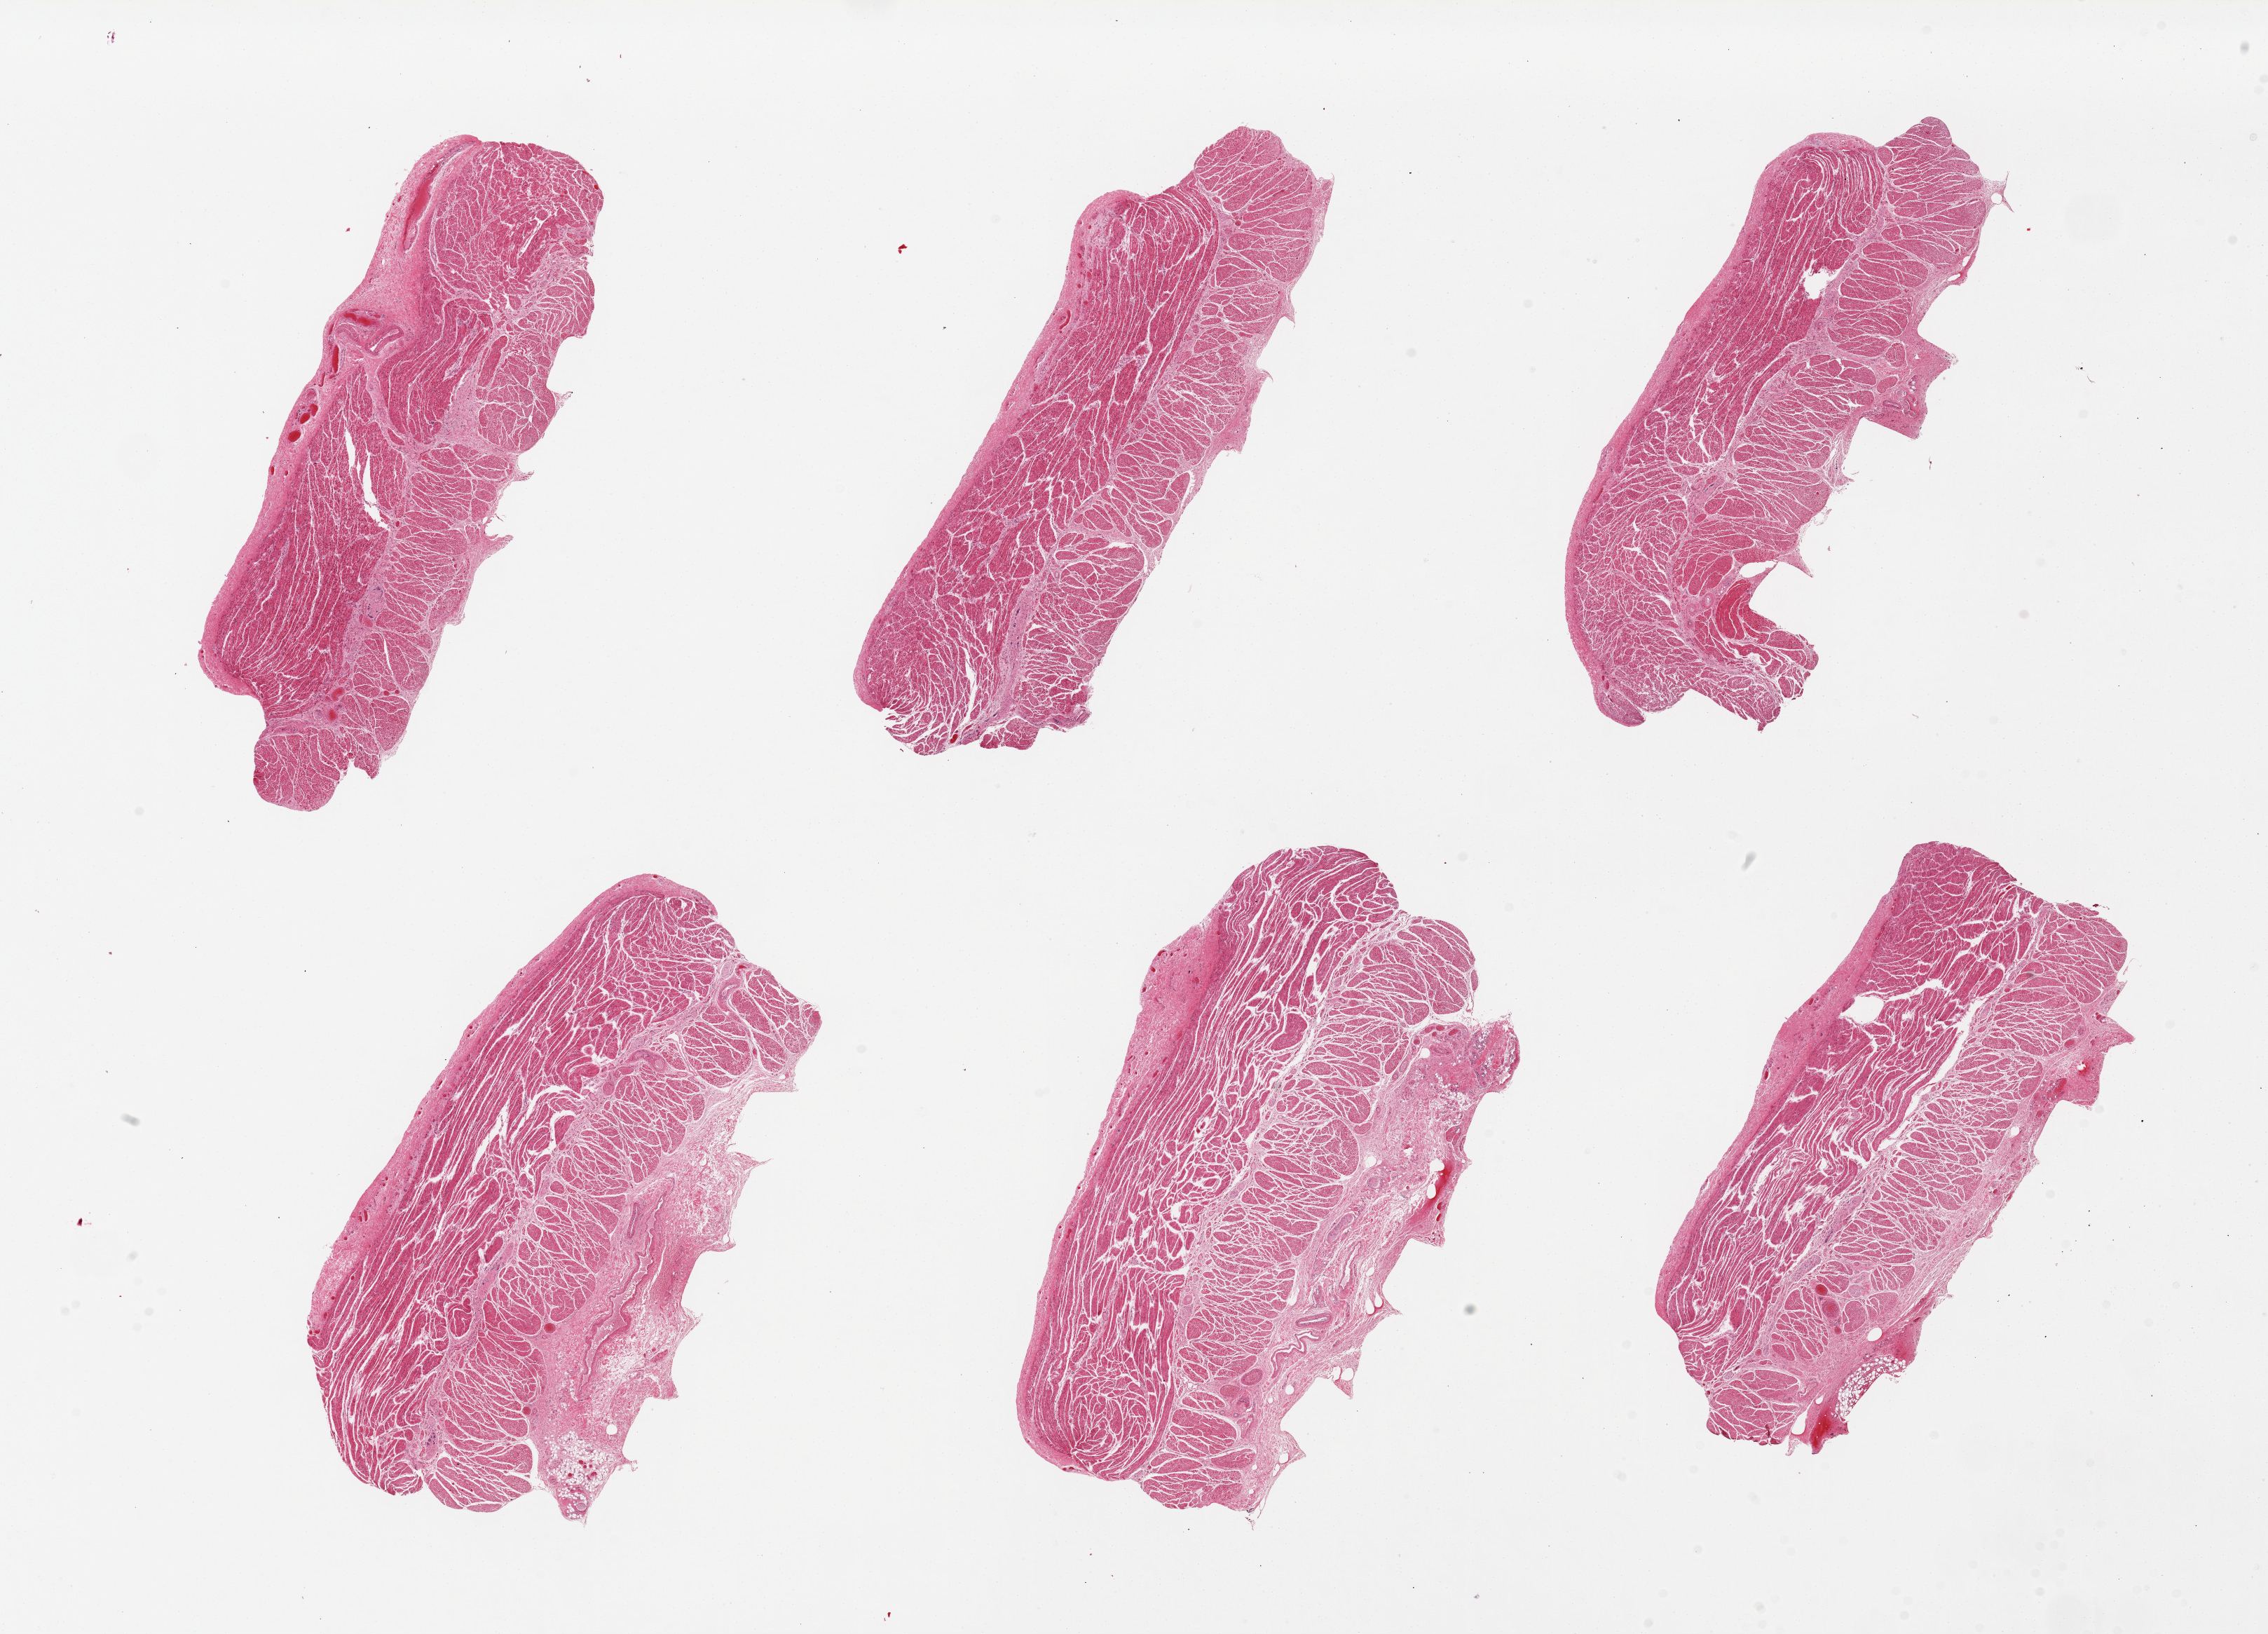
Digitized hematoxylin and eosin (H&E)-stained section, shown as a low-resolution overview of the whole scanned area (about 25.6 x 18.4 mm); PAXgene-fixed paraffin-embedded (PFPE) section; section of esophageal muscle (target tissue); tissue donor sample. Donor sex: male.
- review note (as recorded): 6 pieces; no residual mucosa